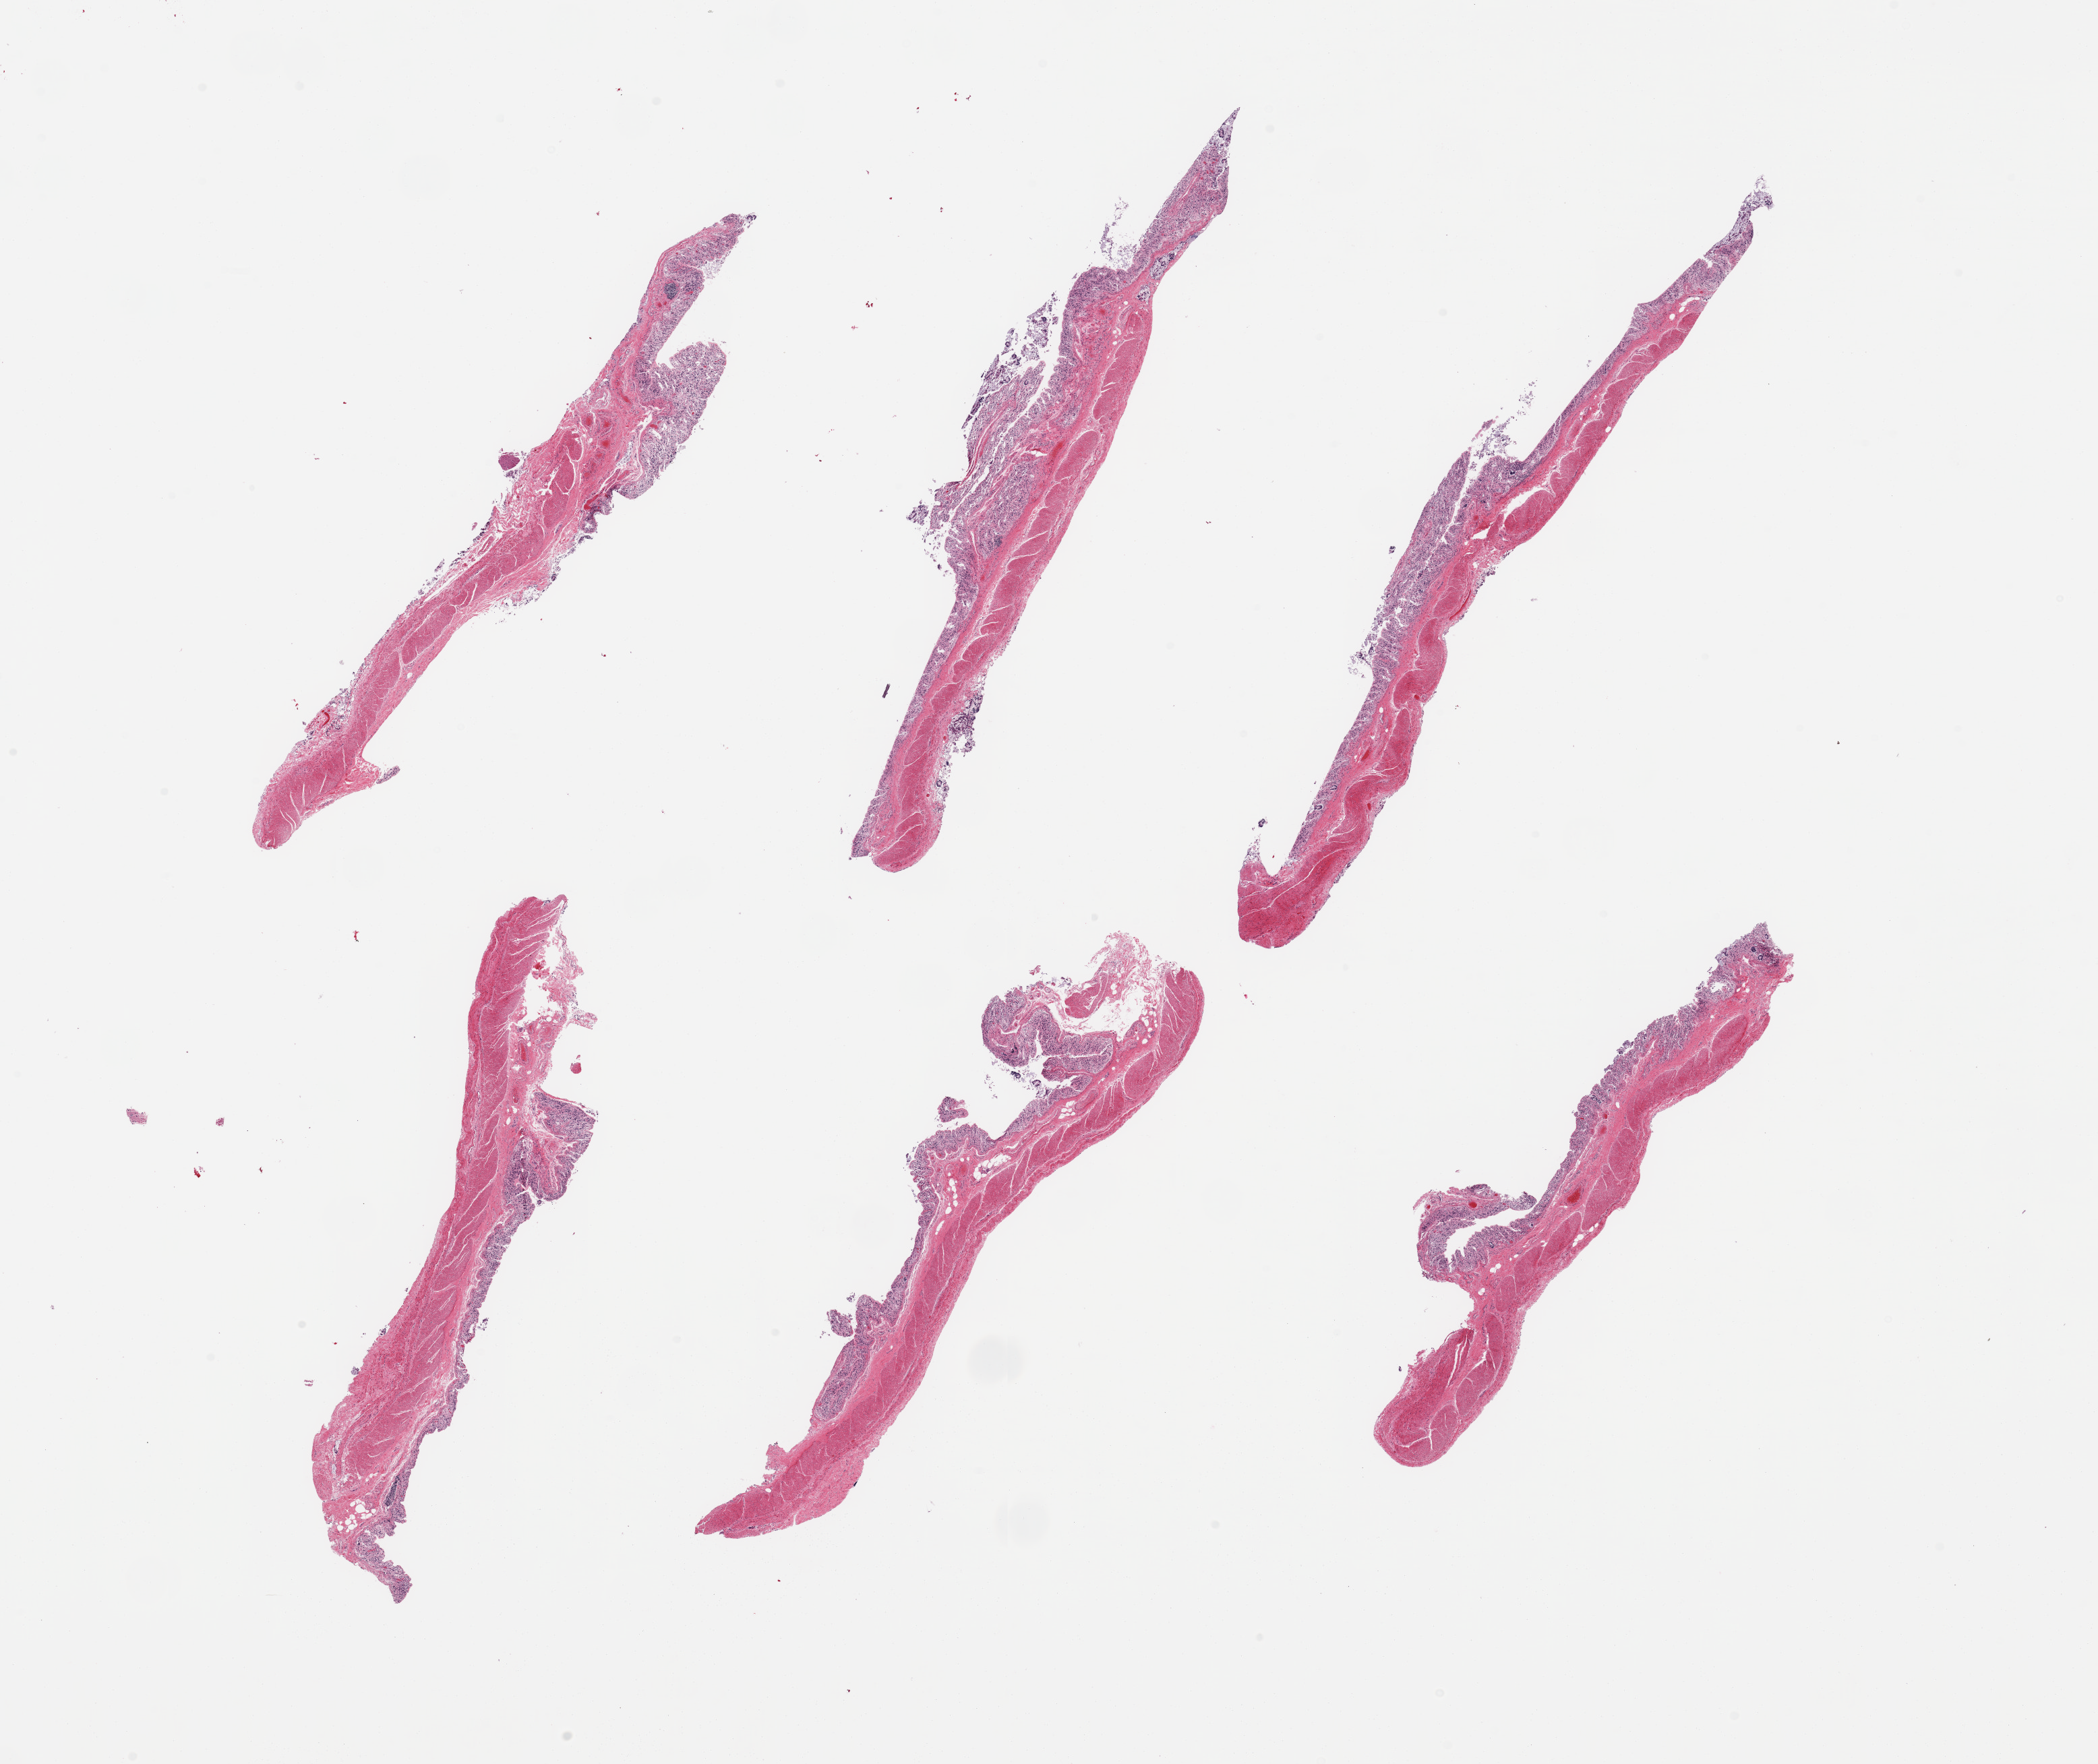
Whole-slide image, H&E stain, brightfield — low-resolution overview of the scanned area, about 24.6 x 20.7 mm (acquisition: 20x scan). PAXgene-fixed, paraffin-embedded tissue. Target tissue: transverse colon. Tissue donor sample. Donor sex: male.
Review note (as recorded): 6 pieces; autolyzed mucosa; intact muscularis.